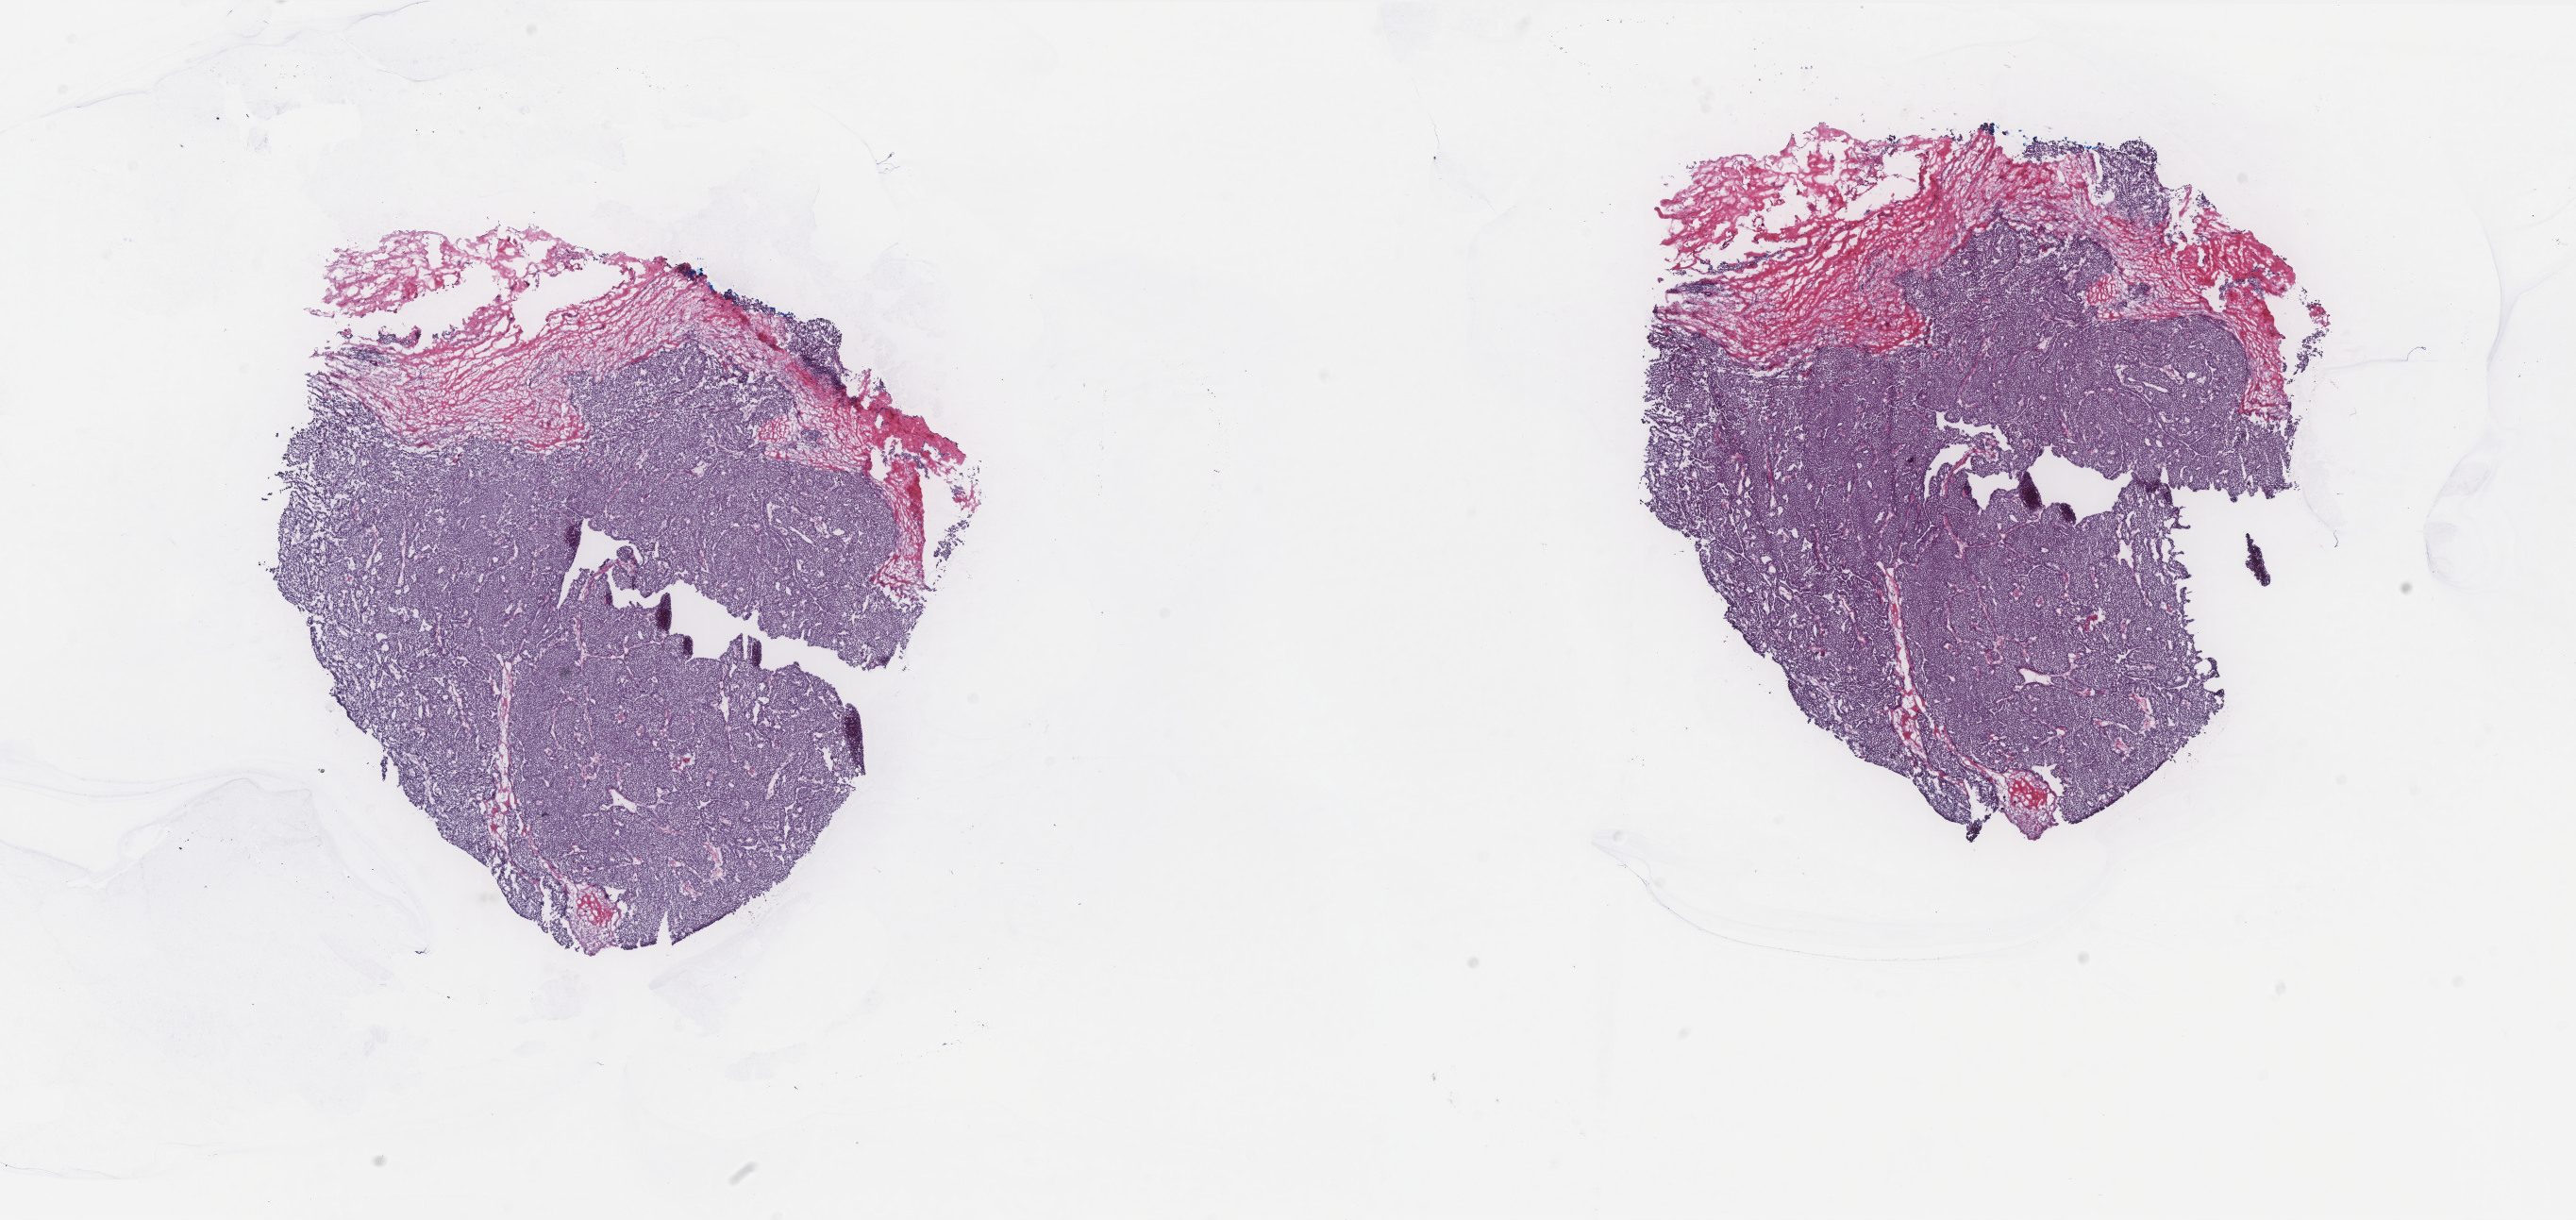
H&E whole-slide image — whole scanned area (about 21.9 x 10.4 mm) shown as a low-resolution overview. Frozen section from the top of the tissue portion. Primary tumour sample from the breast. Patient: female, age at initial diagnosis 77 years. Composition of this section per pathologist review: tumour cells 85%, tumour nuclei 85%, normal cells 0%, stromal cells 15%, necrosis 0%. Infiltration values recorded for this section: lymphocyte infiltration 1%, monocyte infiltration 1%, neutrophil infiltration 0%.
• diagnosis: Intraductal papillary adenocarcinoma with invasion
• TNM: T1c N0 M0
• AJCC pathologic stage: IA (7th edition)